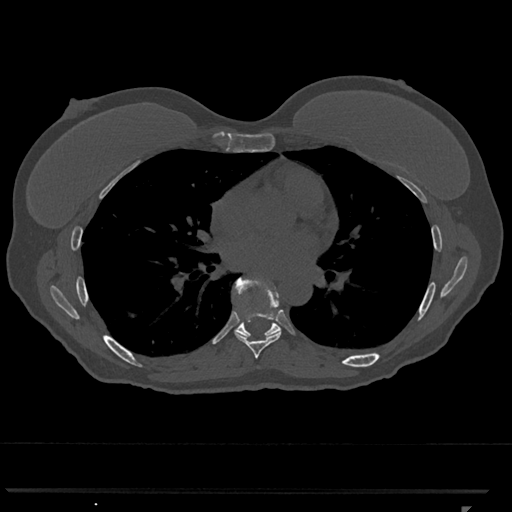
CT including the spine, one axial slice; 120 kVp; bone window (W 1800 / L 400 HU); 0.5 mm slice thickness; 512 × 512 image matrix, field of view 380 × 380 mm. Patient: female, 62 years. From the clinical record (not read from this slice): primary cancer: renal.
Outlined on this slice (semi-automatic segmentation, software-assisted and operator-edited):
- T7 vertebra: bounding box (x1, y1, x2, y2) in pixels: (234, 277, 281, 359)
- T8 vertebra: (233, 277, 281, 337)